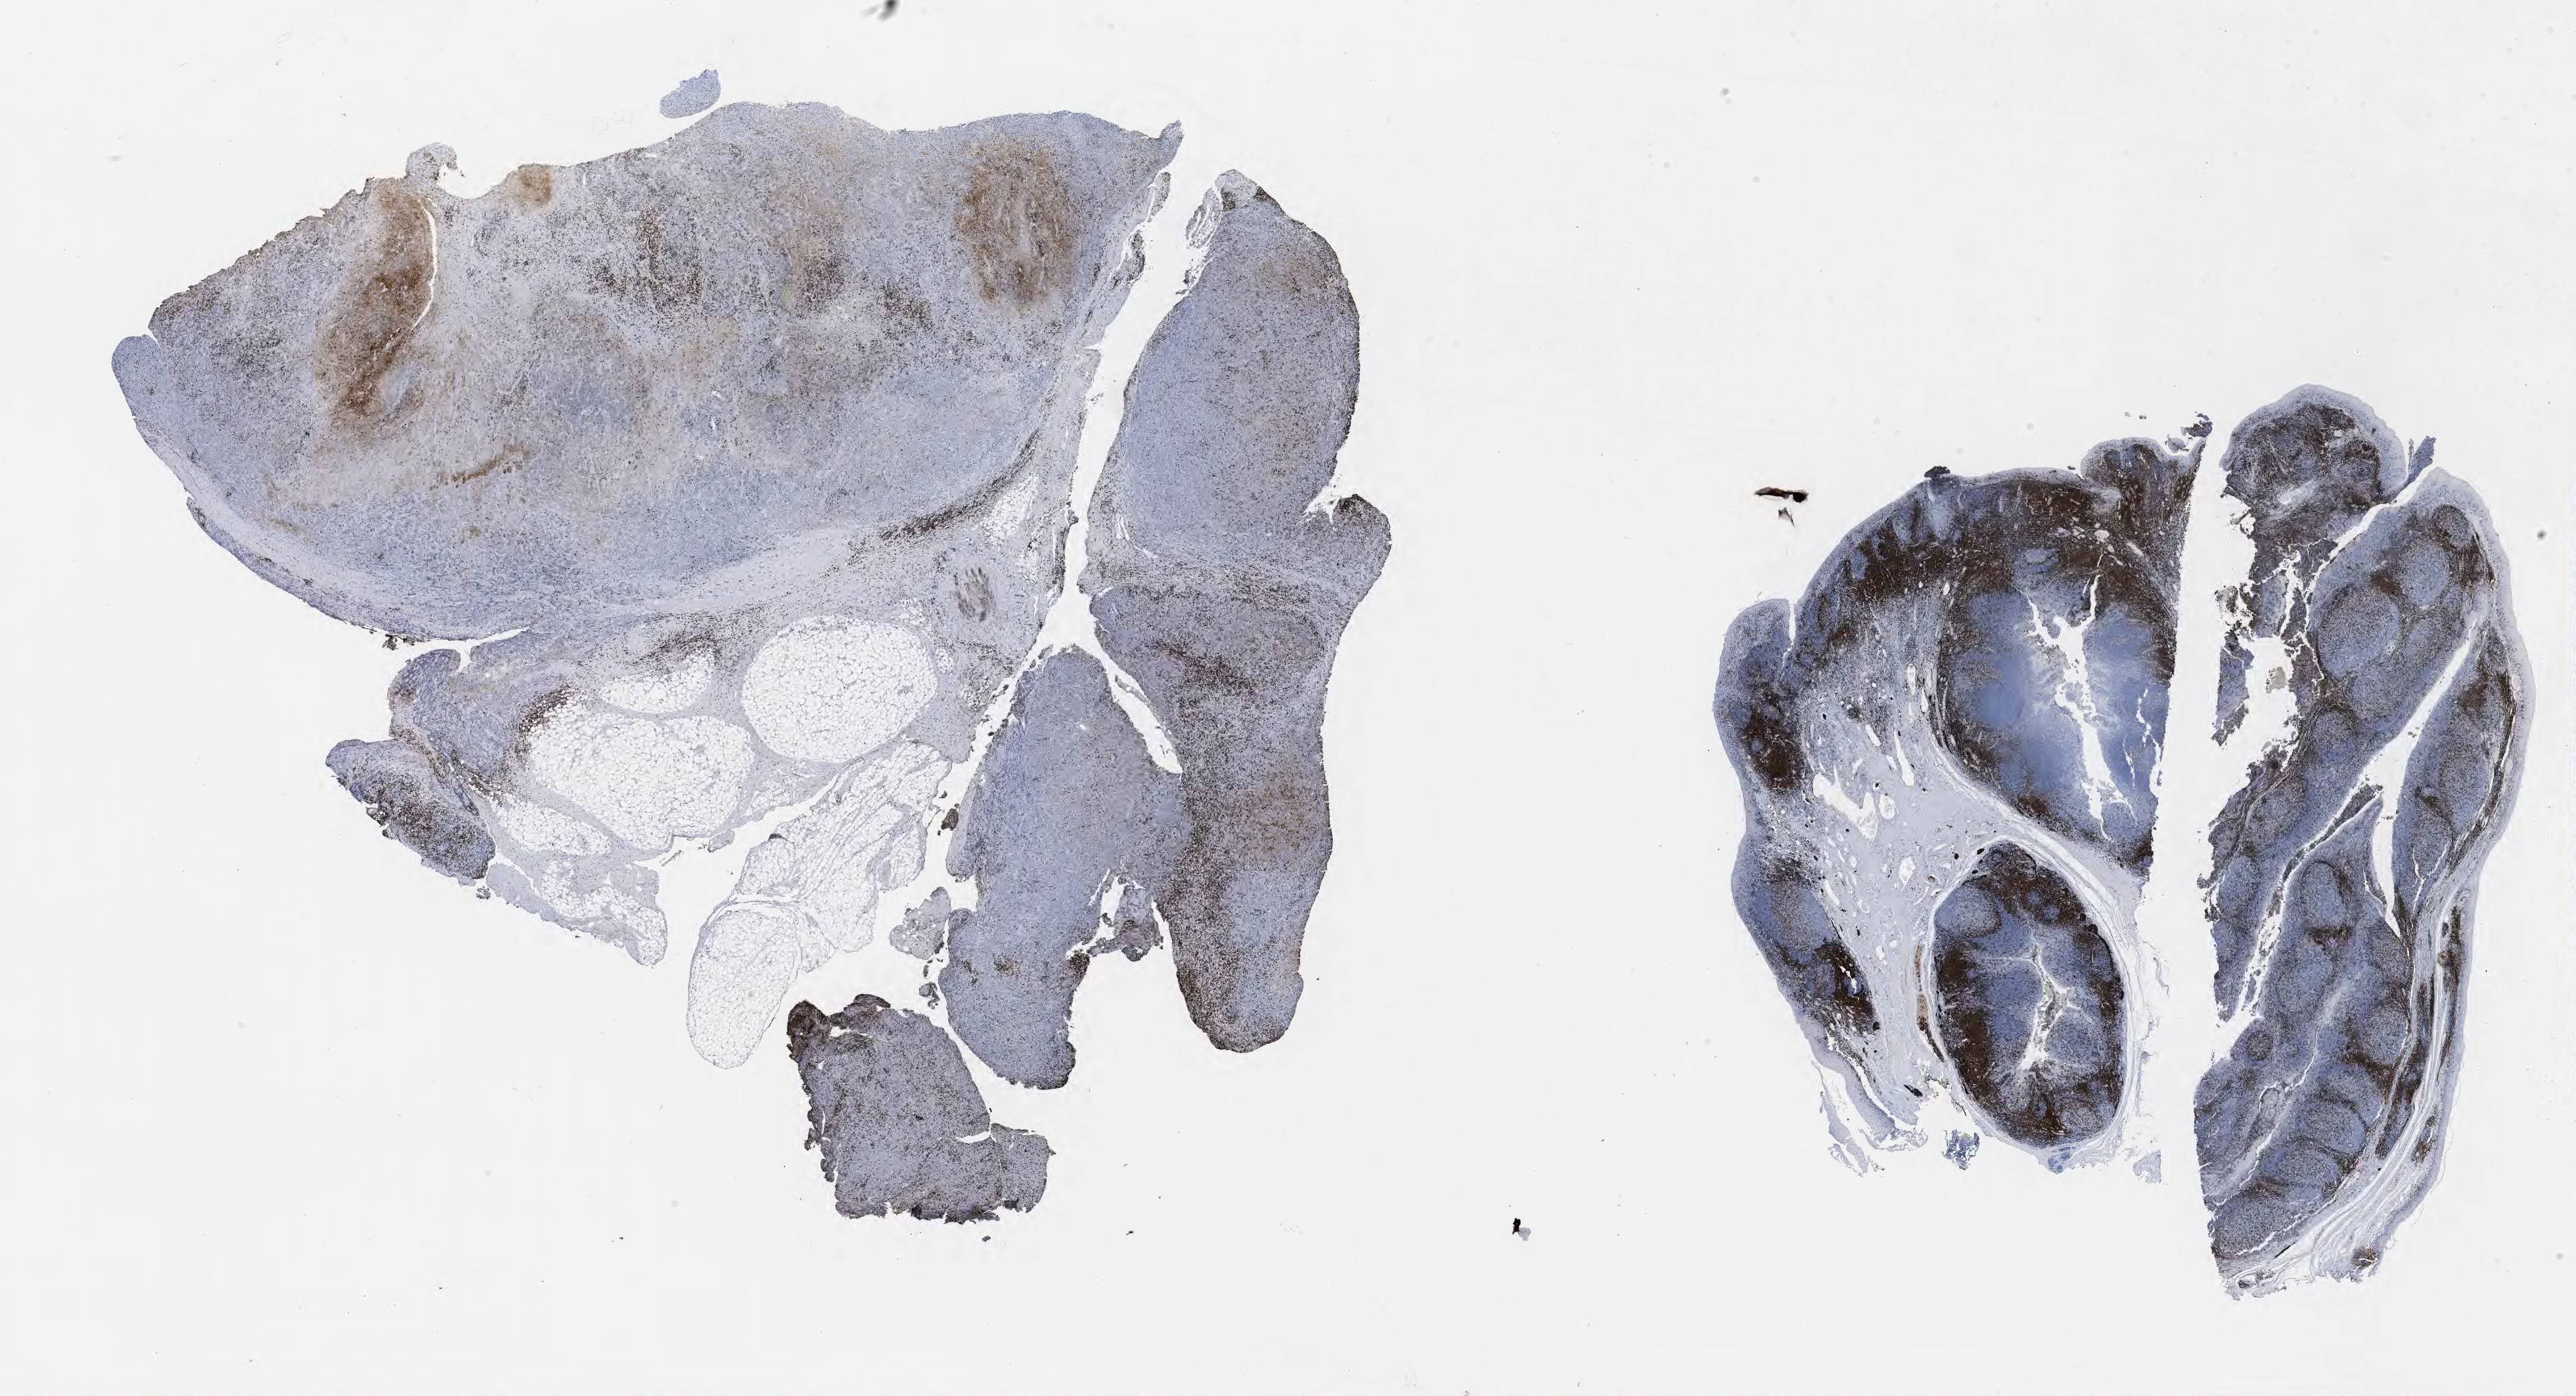
Whole-slide image, immunohistochemical stain for CD3, a low-resolution overview of the entire scanned area, about 31.7 x 17.2 mm. Tumor tissue. Patient female; aged 46.
Histologic diagnosis: Diffuse large B-cell lymphoma, NOS.